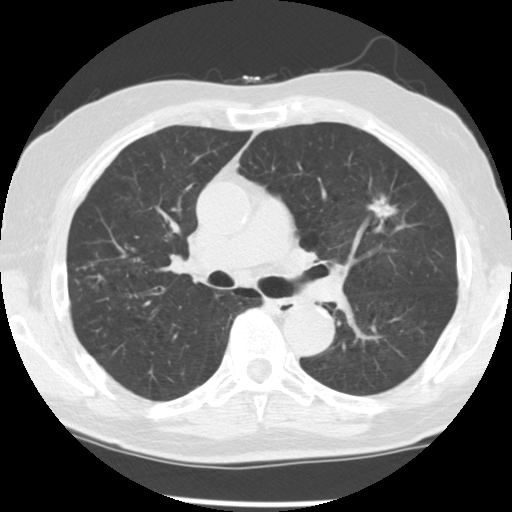
Low-dose screening chest CT, one axial slice; slice 78 of 131 in the series (ordered by position); lung window (W 1500 / L -600 HU); 512 × 512 image matrix.
Structures marked on this image (manually delineated by an expert):
- lesion 1 (tumor, upper lobe of left lung): bounding box <368,196,396,220> (left, top, right, bottom; pixels)